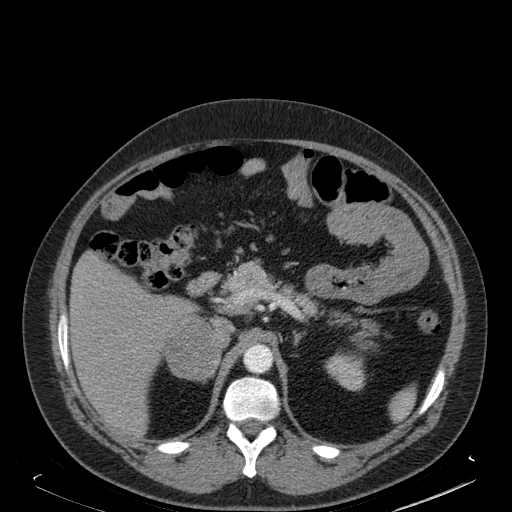
Contrast-enhanced abdominal CT, one axial slice; slice 115 of 181 in the series (ordered by position); soft-tissue window (W 400 / L 40 HU); 512 × 512 image matrix, field of view 405 × 405 mm. Male patient. Case-level facts recorded for this patient, not image findings: diagnosis: adrenocortical carcinoma; tumour side: right adrenal; tumour size at pathology: 7.5 cm; Ki-67 index: 25 %; stage (as recorded): 4.
Outlined on this slice (semi-automatic segmentation, software-assisted and operator-edited):
- mass: box from (x=165, y=319) to (x=221, y=378) px